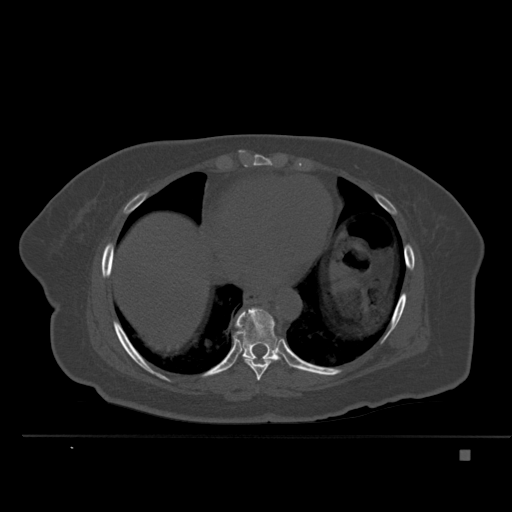
CT including the spine, one axial slice. Slice 304 of 477 in the series (ordered by position). Bone window (W 1800 / L 400 HU). 1.5 mm slice thickness. 512 × 512 image matrix, field of view 422 × 422 mm. Female patient, age 74 years. From the clinical record (not read from this slice): primary cancer: colon.
Annotated regions visible in this slice (semi-automatic segmentation, software-assisted and operator-edited):
- T8 vertebra: bounding box [x1, y1, x2, y2] px = [245, 359, 271, 381]
- T9 vertebra: [234, 307, 291, 367]